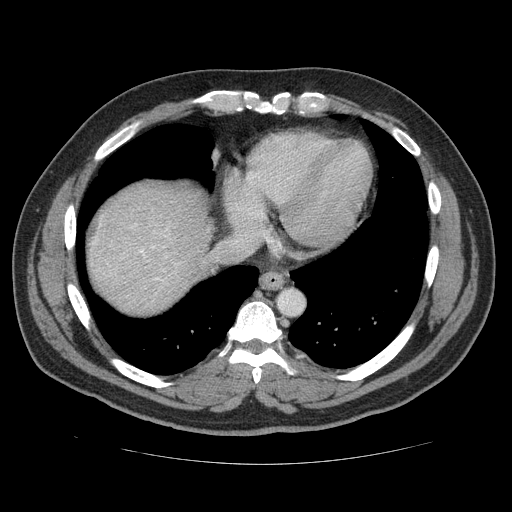
Contrast-enhanced abdominal CT (liver protocol), one axial slice; slice 107 of 113 in the series (ordered by position); reconstruction kernel STANDARD; soft-tissue window (W 400 / L 40 HU); 2.5 mm slice thickness; 512 × 512 image matrix, field of view 400 × 400 mm. From the clinical record (not read from this slice): diagnosis: hepatocellular carcinoma (patient treated with transarterial chemoembolisation; whether this scan precedes or follows treatment is not stated here); TNM stage (as recorded): Stage-II; Child-Pugh class: B; tumour differentiation: moderately differentiated; tumour nodularity: multinodular.
Structures marked on this image (semi-automatically segmented with operator editing):
- abdominal aorta: bounding box [x1, y1, x2, y2] px = [279, 291, 302, 315]
- liver parenchyma outside the tumour (the mass and vessels are separate outlines, so this box may not span the whole liver): [88, 182, 205, 308]